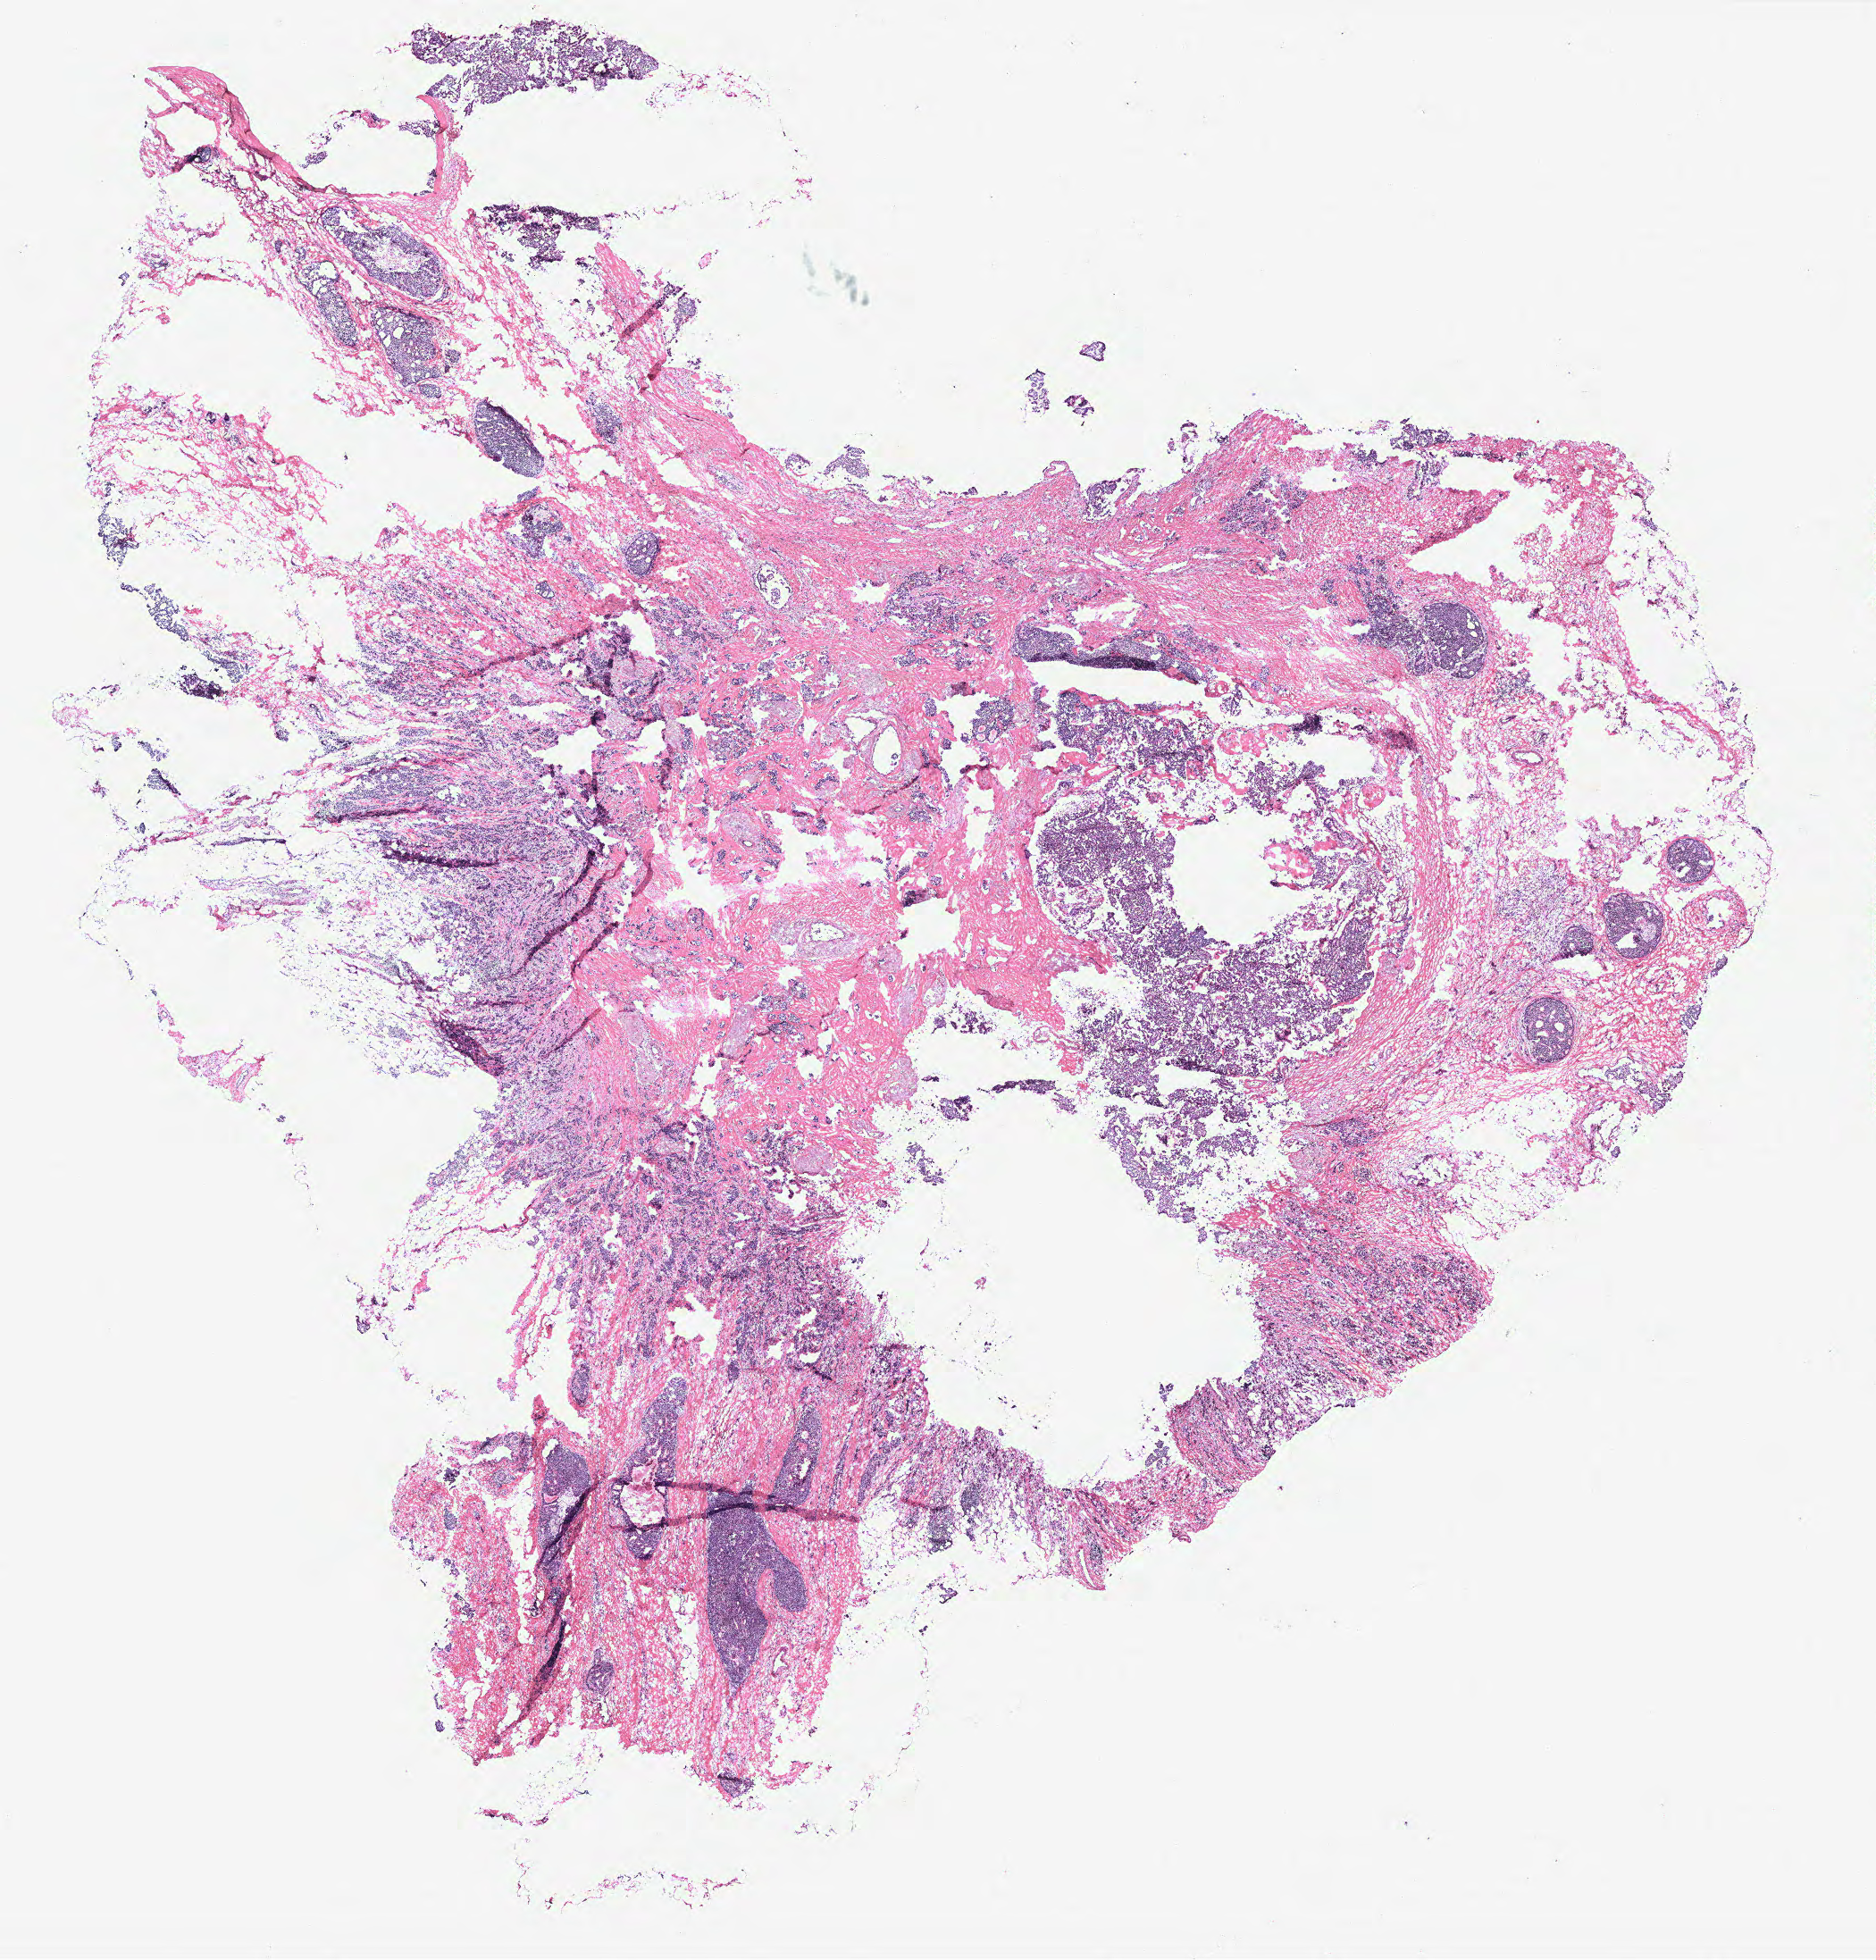
Digitized H&E-stained tissue section (whole slide), a low-resolution overview of the entire scanned area, about 16.8 x 17.6 mm (slide scanned at 40x), tumour tissue sample, breast. 67-year-old female patient.
AJCC pathologic stage: IIIA. Histologic diagnosis: Infiltrating duct carcinoma, NOS.